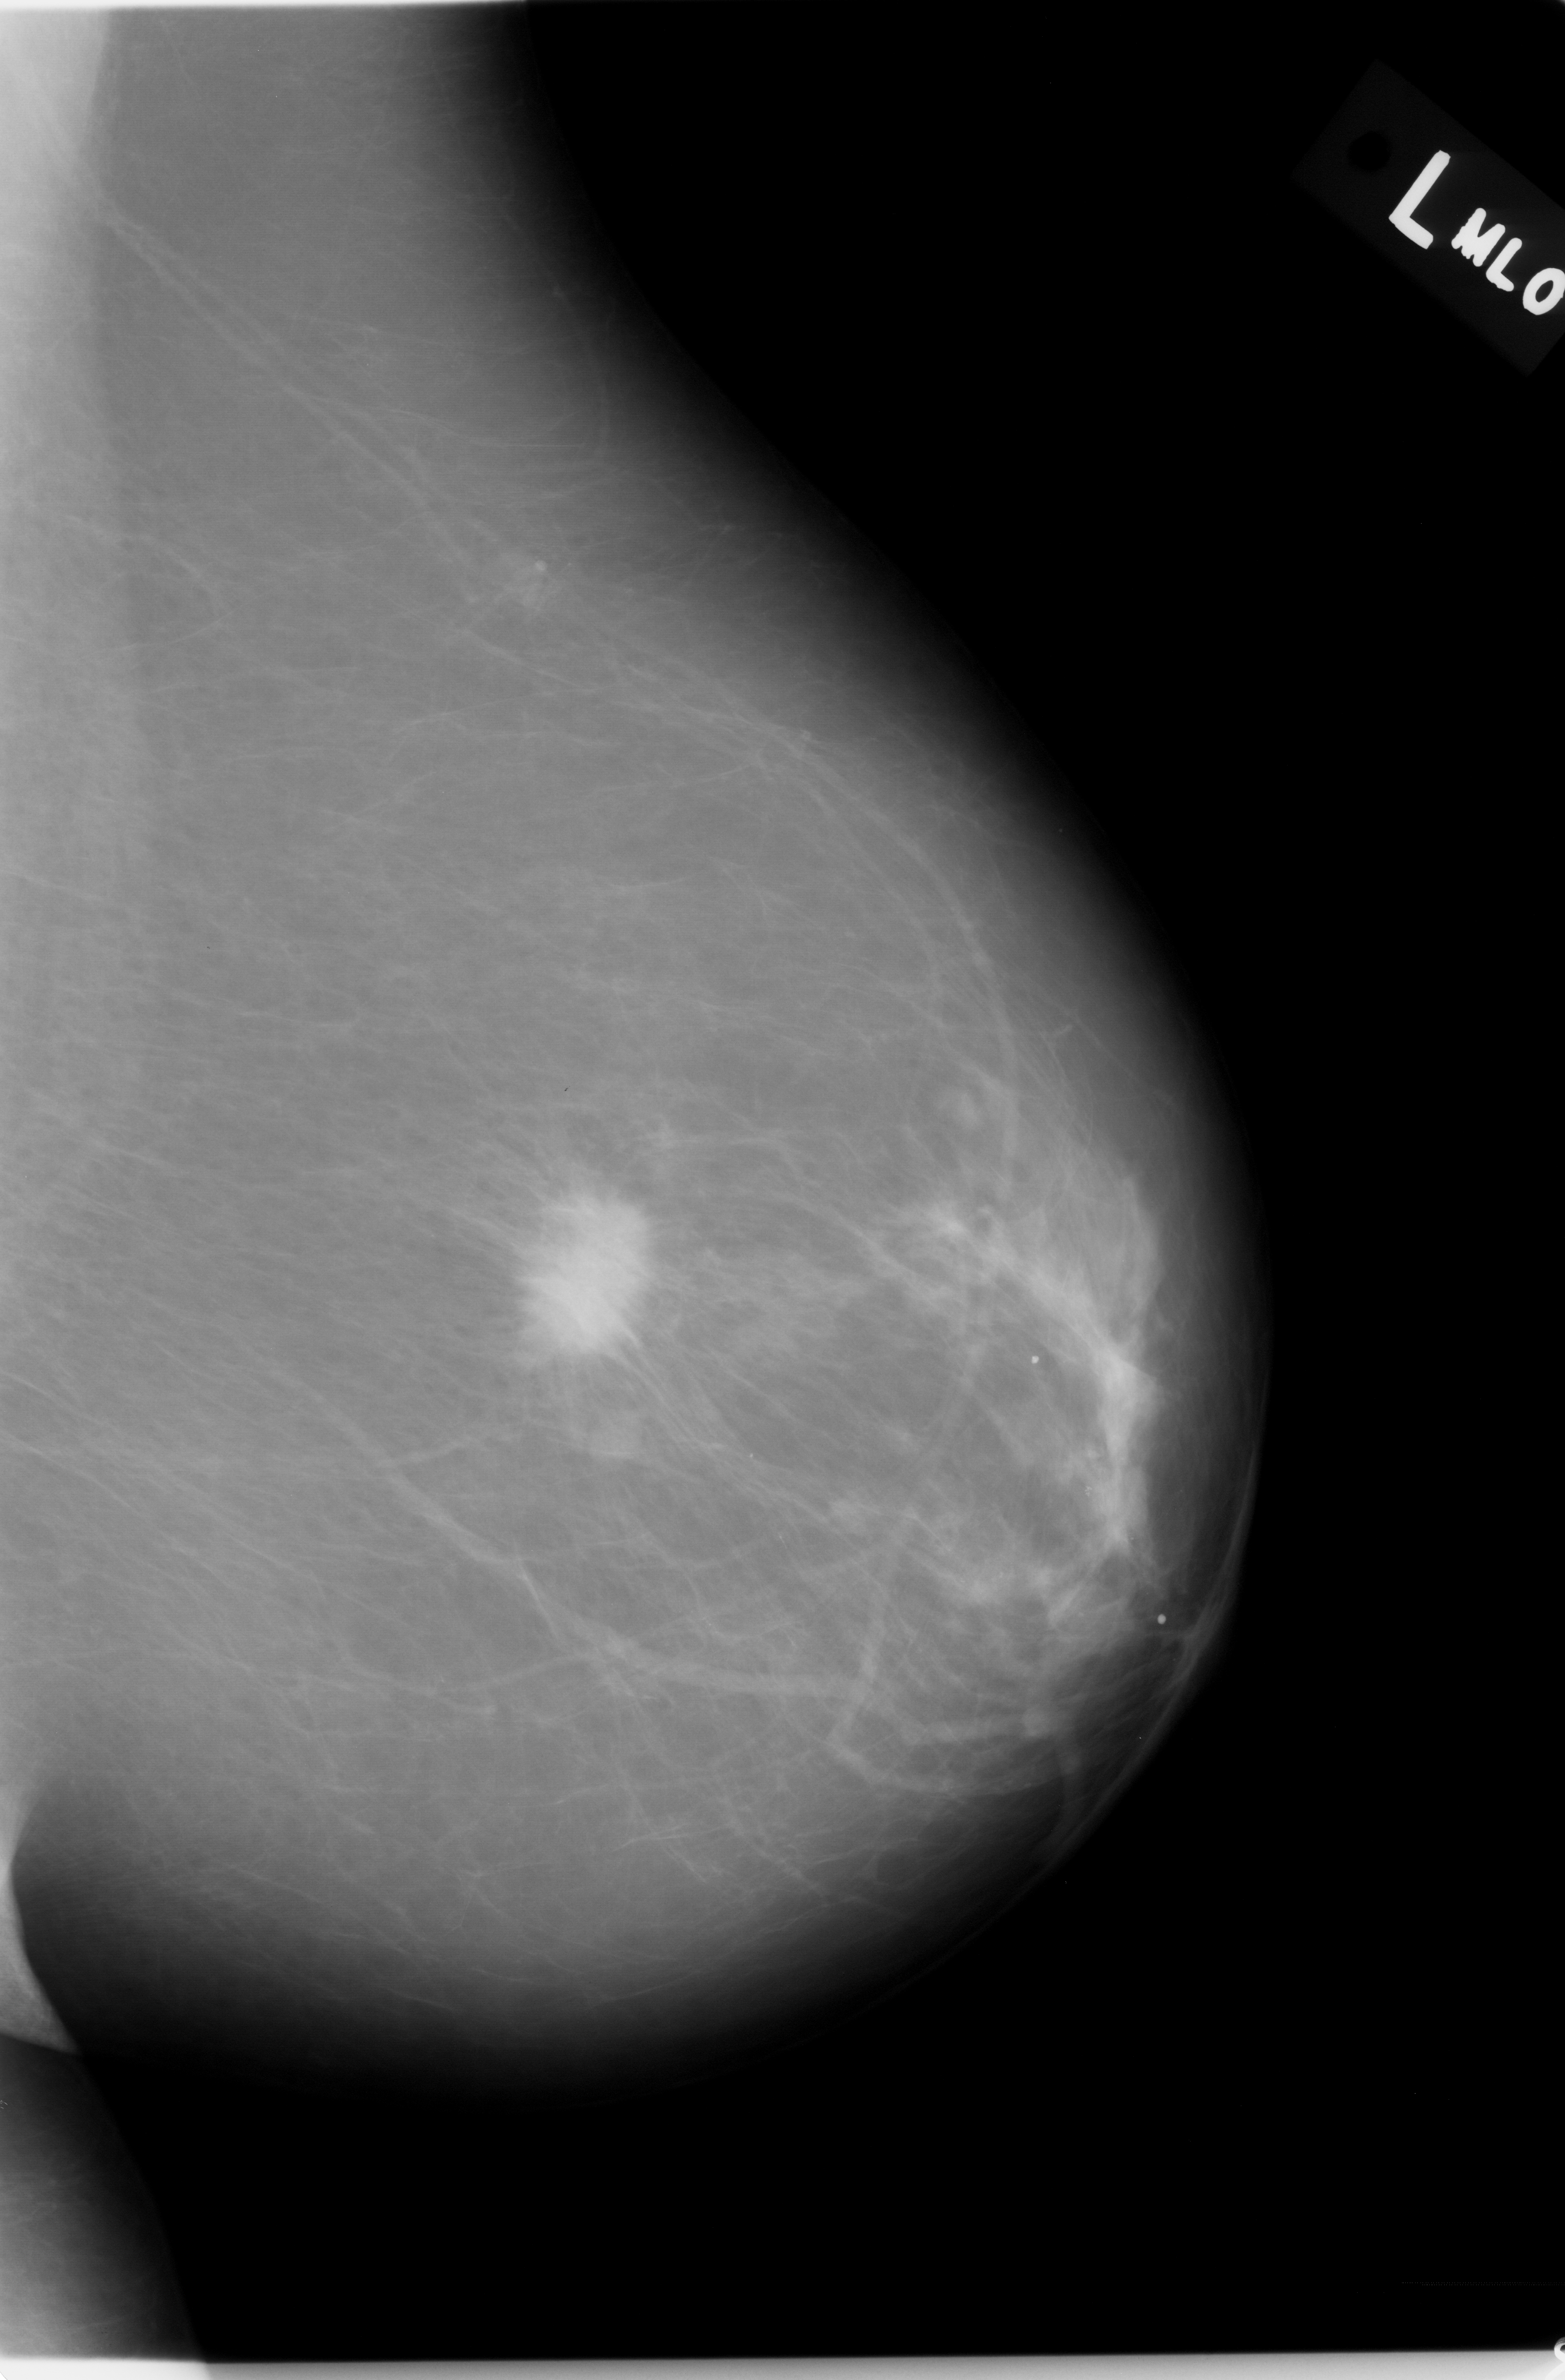
Scanned film-screen mammogram. Left breast. Mediolateral oblique (MLO) view. Breast composition: almost entirely fatty (BI-RADS density category 1 of 4). 1565 × 2380 image matrix.
Expert-marked regions of interest on this film, with their recorded descriptors:
- mass, shape irregular, margins spiculated; BI-RADS assessment category 5; subtlety rating 5 on a 1 (subtle) to 5 (obvious) scale; pathology (as recorded): malignant: box from (x=493, y=1188) to (x=670, y=1414) px